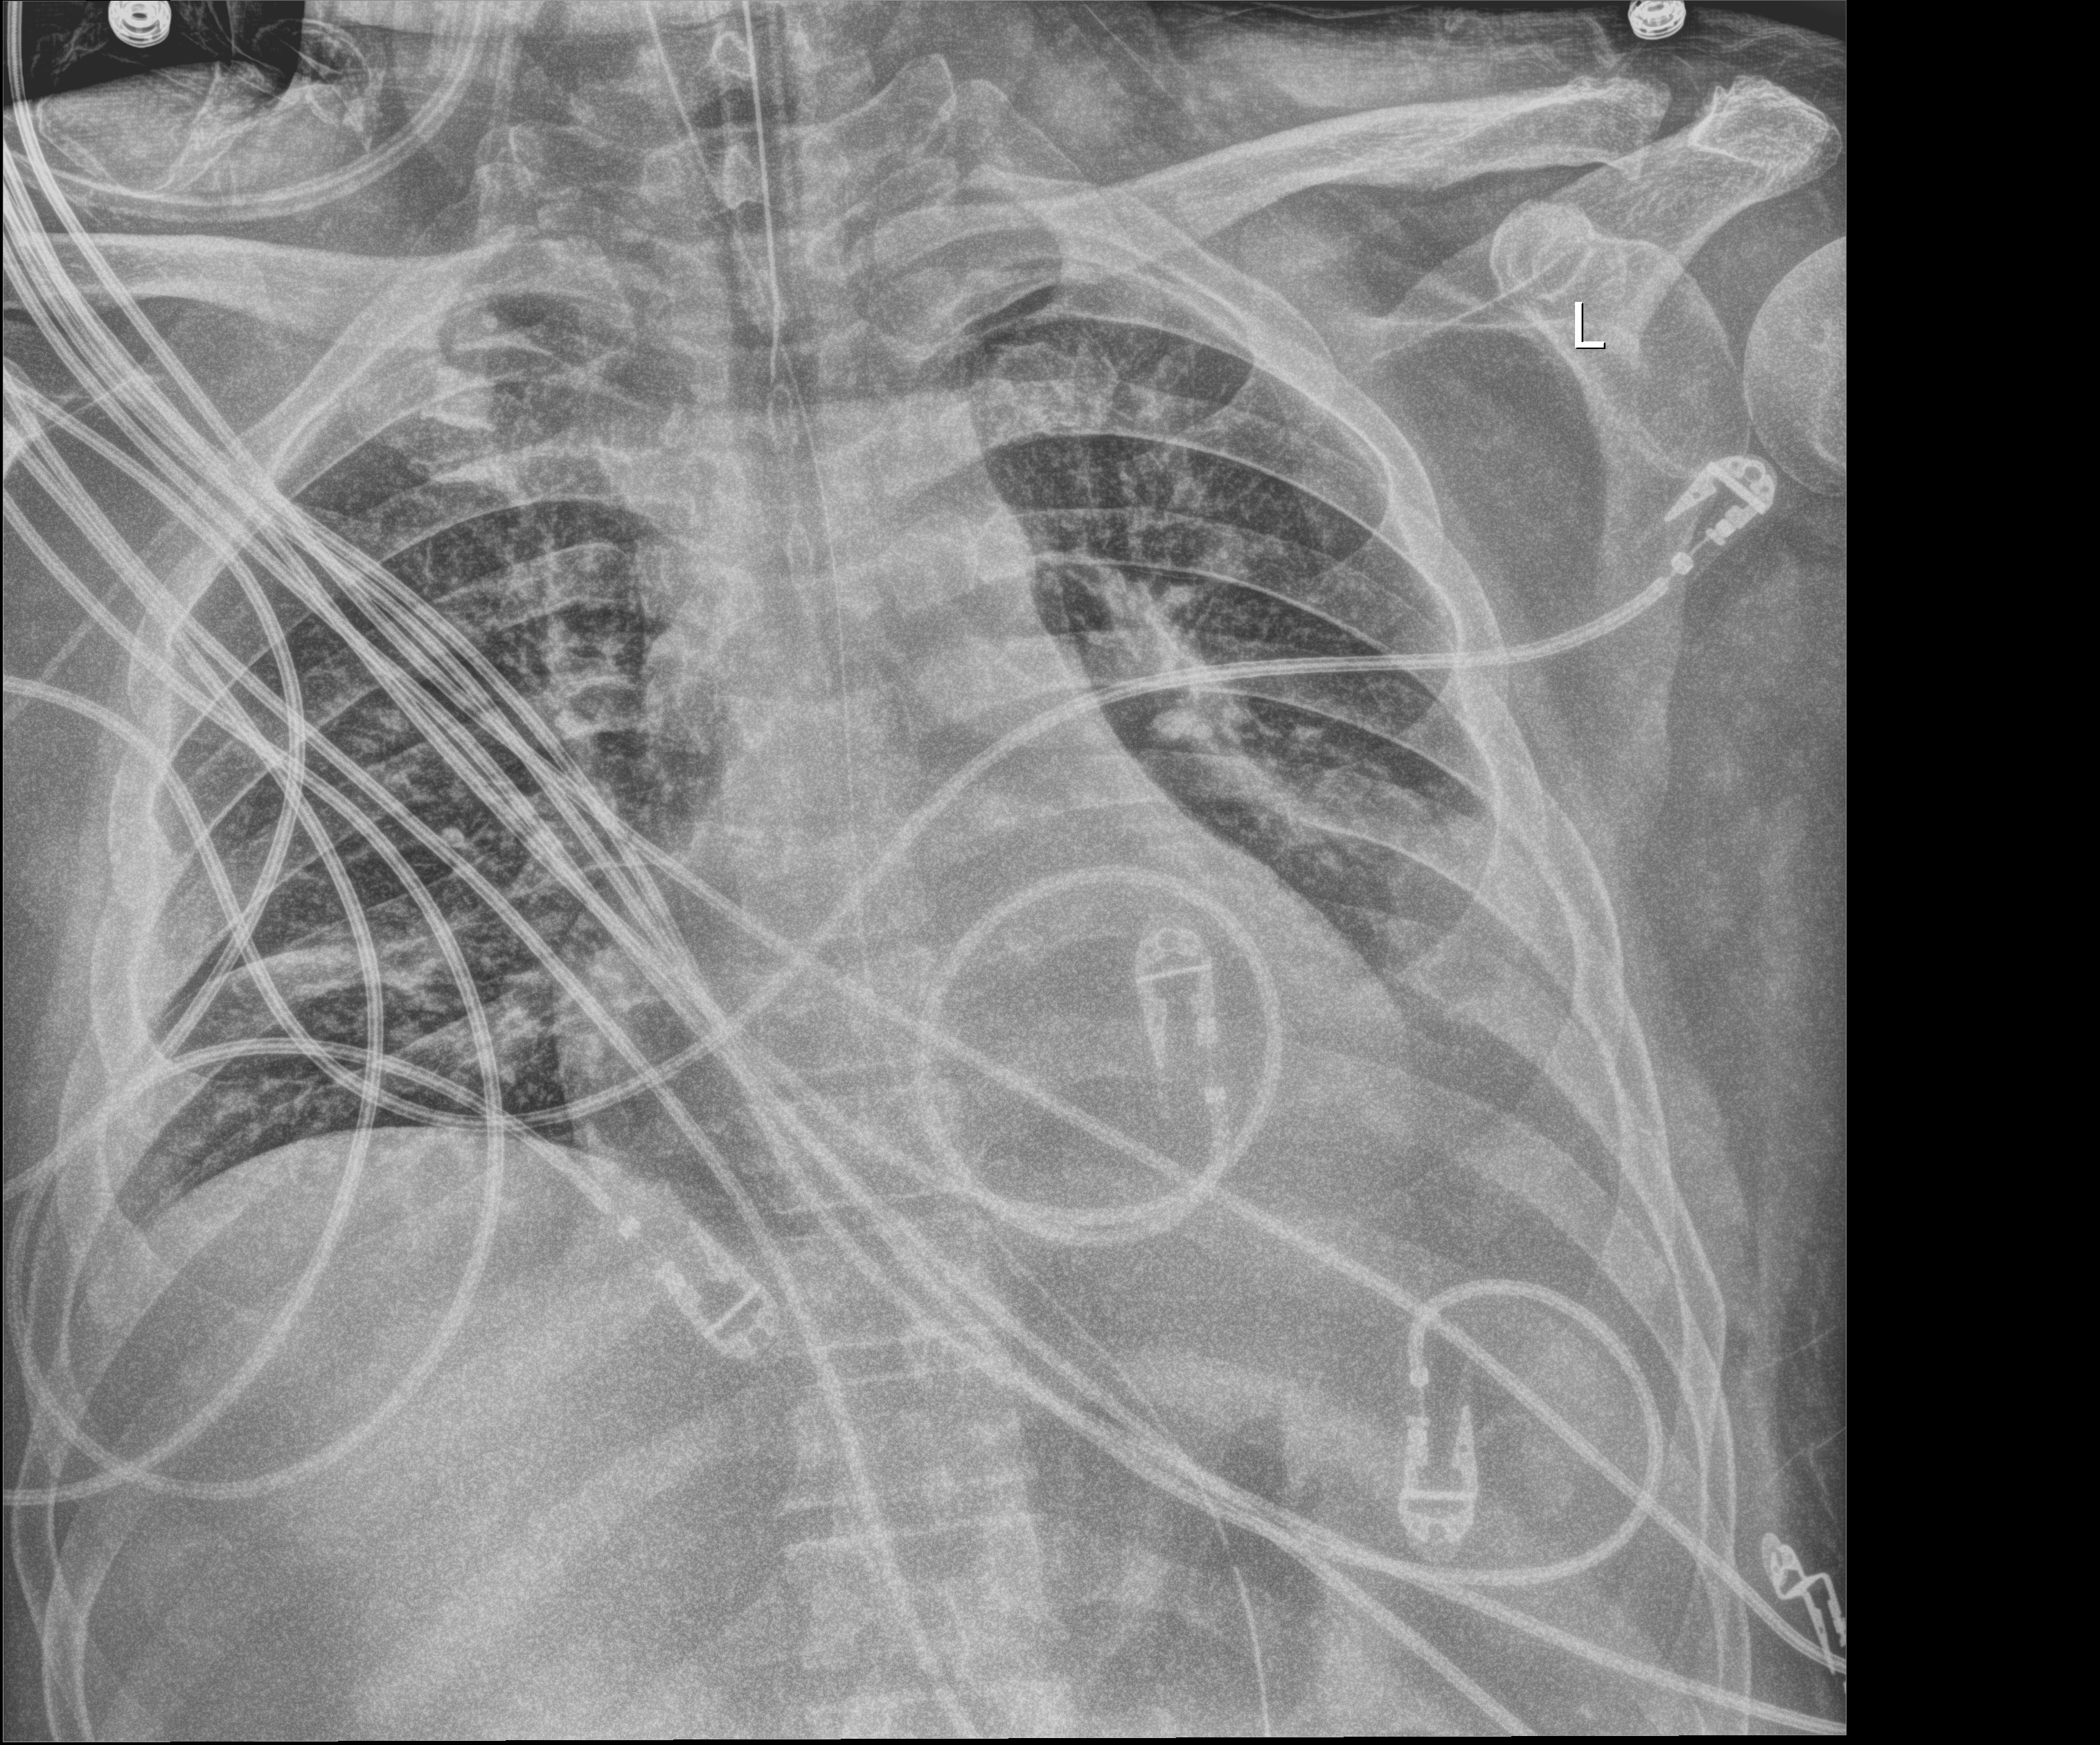
Chest X-ray; anteroposterior (AP) projection. Male patient hospitalised with COVID-19, age 18–59 years.
Admission-level facts for this patient (not findings on this image; timing relative to this image not recorded): admitted to intensive care during this hospital stay: yes; mechanically ventilated during this hospital stay: yes.